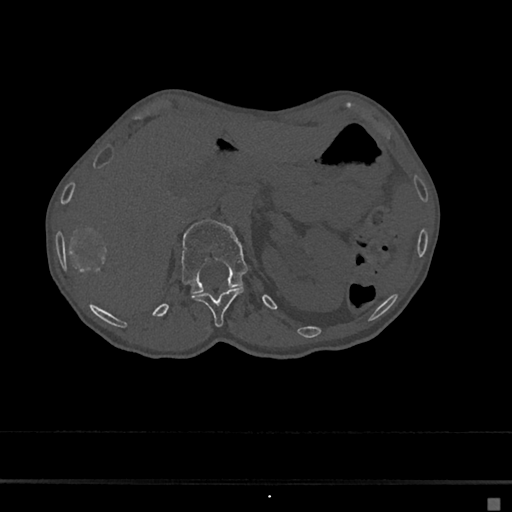
CT including the spine, one axial slice. Position 89 of 797 along the scan axis. 120 kVp. Bone window (W 1800 / L 400 HU). 512 × 512 image matrix, field of view 360 × 360 mm. Patient: female, 68 years. From the clinical record (not read from this slice): primary cancer: renal.
Outlined on this slice (semi-automatic segmentation, software-assisted and operator-edited):
- L1 vertebra: box from (x=181, y=220) to (x=248, y=294) px
- T12 vertebra: (x=192, y=287)–(x=244, y=327)